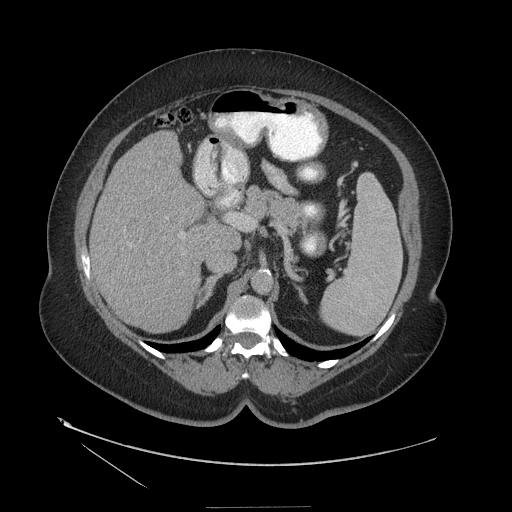
Contrast-enhanced abdominal CT (liver protocol), one axial slice; position 71 of 127 along the scan axis; reconstruction kernel STANDARD; soft-tissue window (W 400 / L 40 HU); 2.5 mm slice thickness; 512 × 512 image matrix, field of view 480 × 480 mm. Case-level facts recorded for this patient, not image findings: diagnosis: hepatocellular carcinoma (patient treated with transarterial chemoembolisation; whether this scan precedes or follows treatment is not stated here); TNM stage (as recorded): Stage-II; Child-Pugh class: A; tumour differentiation: well differentiated; tumour size: 3 cm.
Annotated regions visible in this slice (semi-automatically segmented with operator editing):
- liver parenchyma outside the tumour (the mass and vessels are separate outlines, so this box may not span the whole liver): bounding box <90,132,204,332> (left, top, right, bottom; pixels)